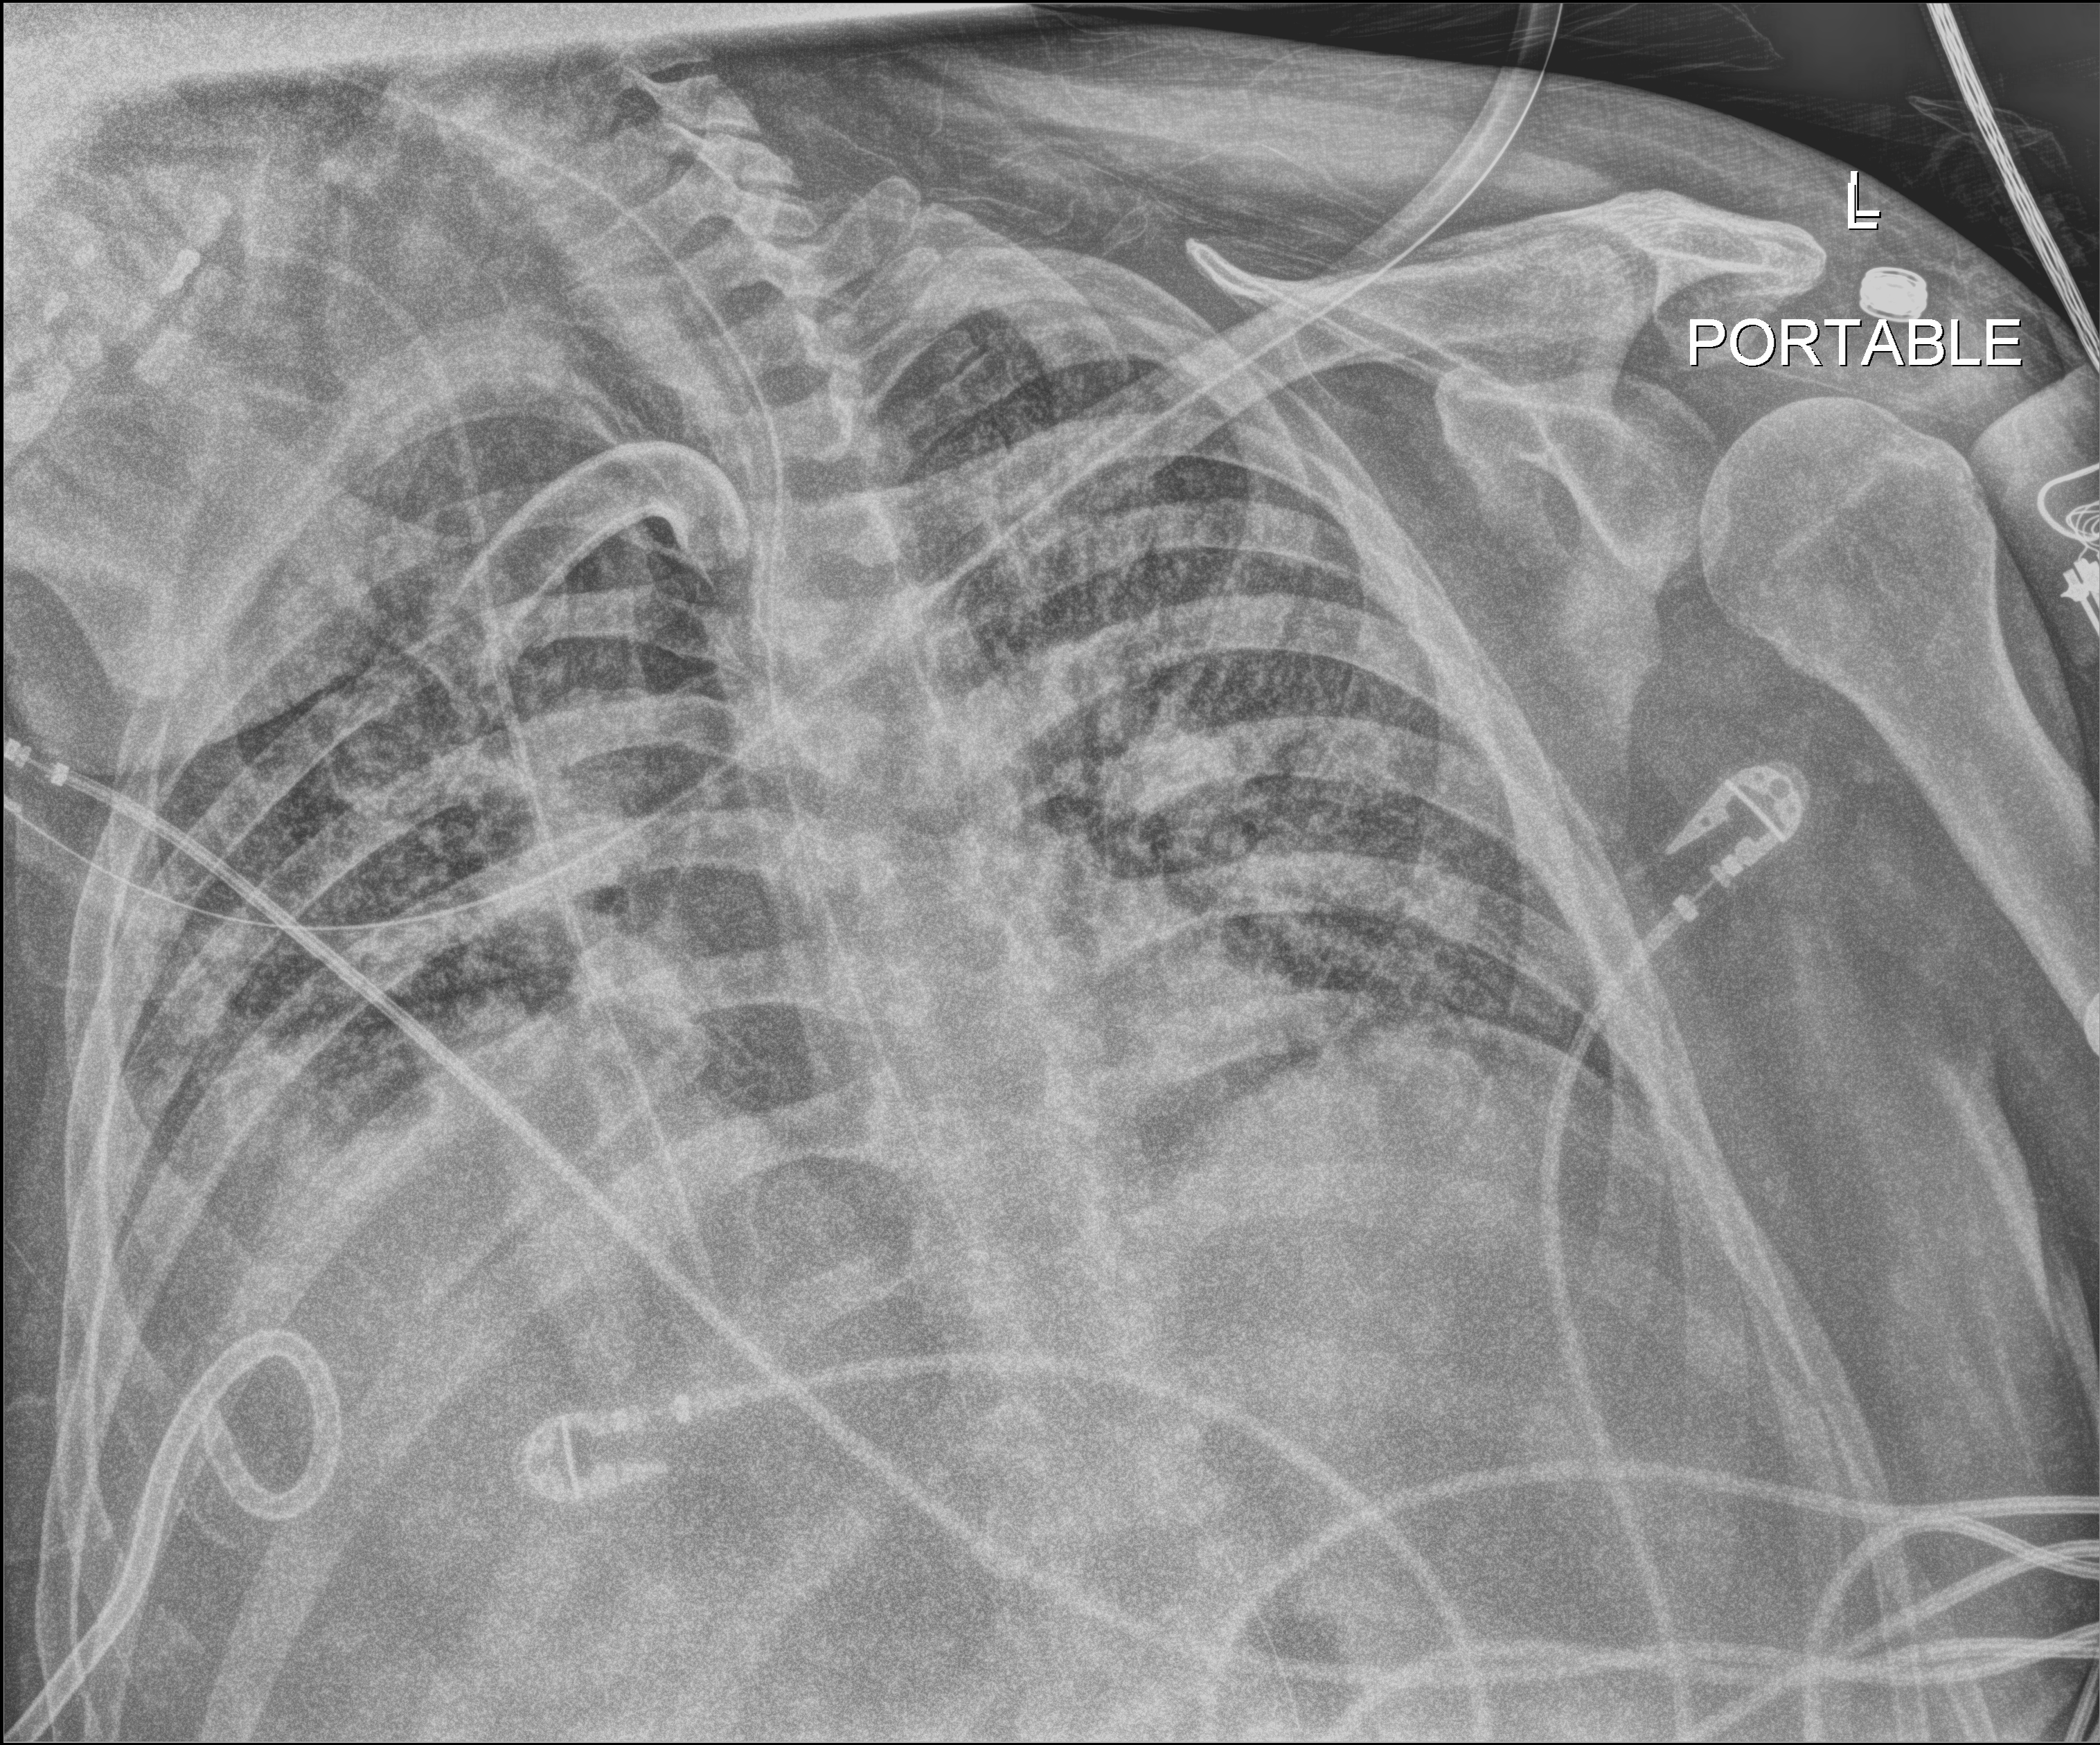
Chest X-ray (portable). Patient hospitalised with COVID-19; male, aged 18–59 years.
Admission-level facts for this patient (not findings on this image; timing relative to this image not recorded): mechanically ventilated during this hospital stay: yes; hypertension (admission record): yes; admitted to intensive care during this hospital stay: yes.